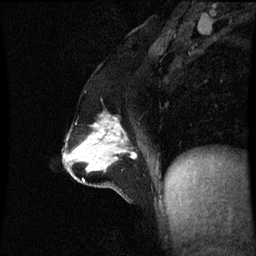
Breast MRI (dynamic contrast-enhanced), one sagittal slice. Slice 31 of 60 in the series (ordered by position). Dynamic contrast-enhanced series, image 2 of 3 at this slice position (ordered by acquisition). 1.5 T. TE 4.2 ms, TR 8.9 ms. 2.1 mm slice thickness. 256 × 256 image matrix, field of view 200 × 200 mm. Female patient, age 47 years. Case-level facts recorded for this patient, not image findings: setting: breast cancer imaged before/during neoadjuvant chemotherapy; receptor status: HR-positive, HER2-negative.
Structures marked on this image (semi-automatic segmentation, software-assisted and operator-edited):
- analysis volume of interest (the breast-tissue region the enhancement analysis was run in; not a lesion): bounding box [x1, y1, x2, y2] px = [71, 116, 138, 163]
- tumour enhancement mask (voxels above the 70 % enhancement threshold inside the analysis volume of interest): [94, 120, 137, 157]